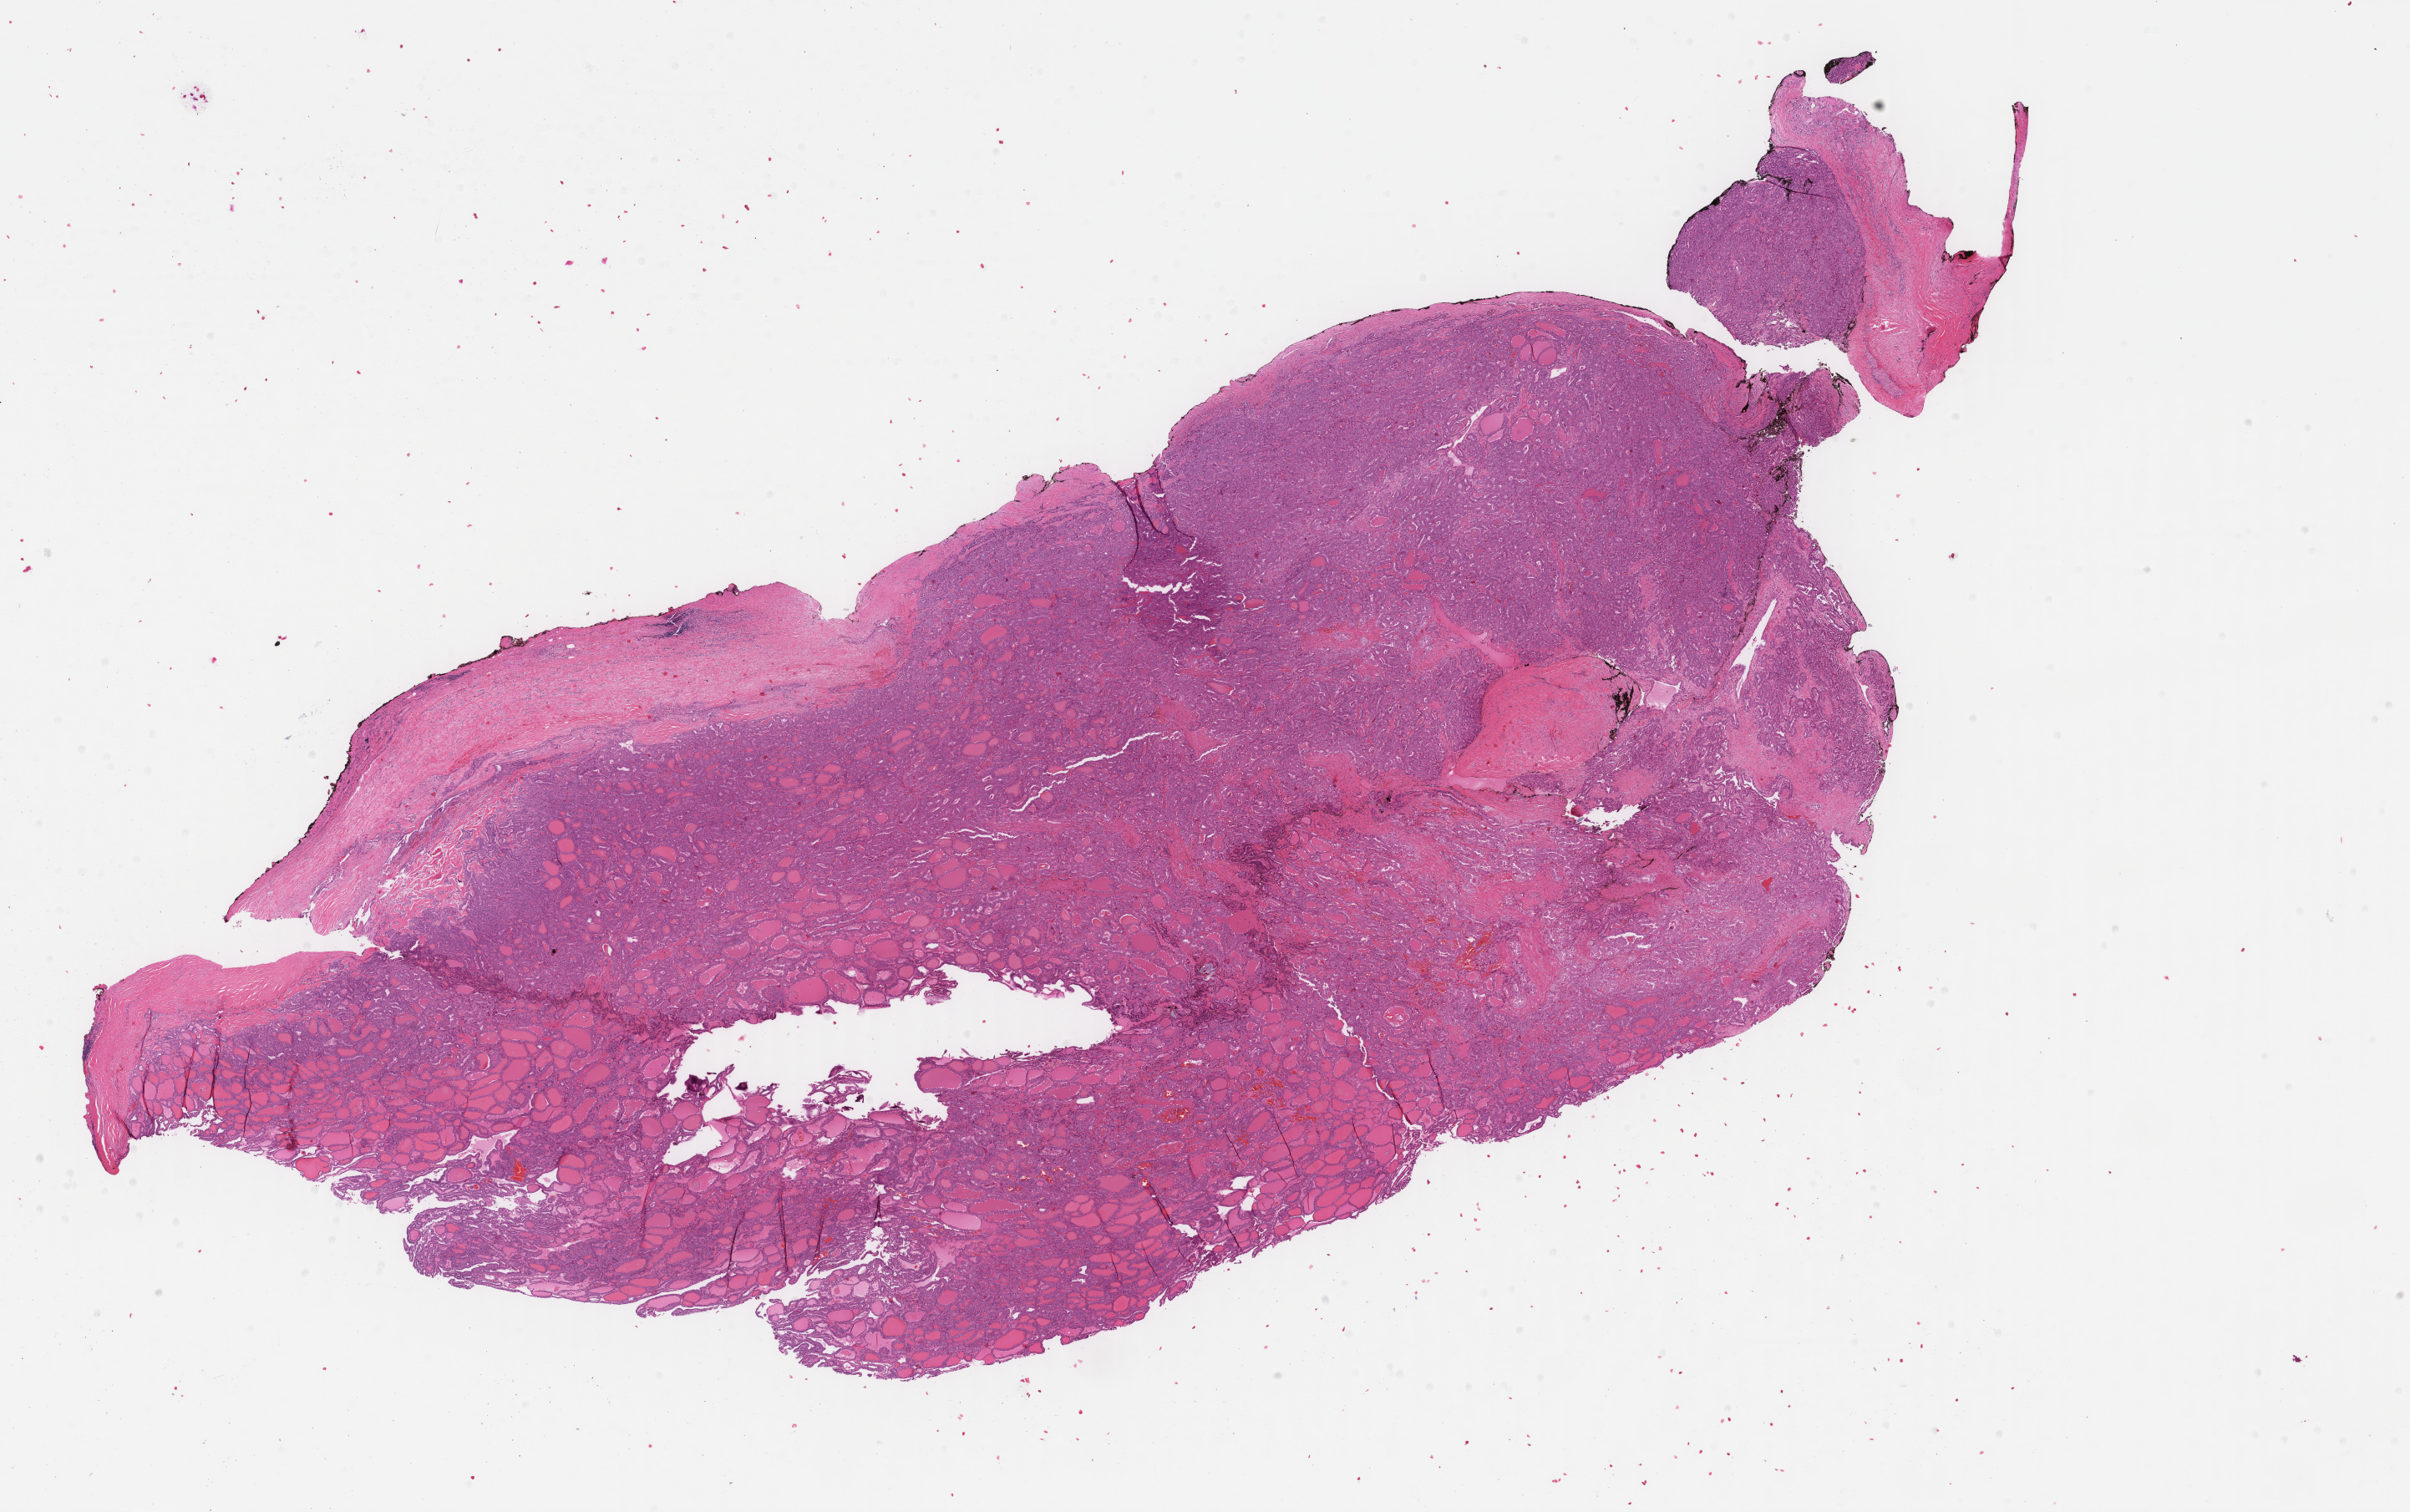
Digitized H&E-stained tissue section (whole slide), a low-resolution overview of the entire scanned area, about 22.9 x 14.4 mm (acquisition: 40x scan). Formalin-fixed paraffin-embedded (FFPE) diagnostic section. Sample: primary tumour, thyroid. Female, age 73 years at initial diagnosis.
• AJCC pathologic stage: III
• laterality: left
• histologic diagnosis: Papillary adenocarcinoma, NOS (thyroid gland)